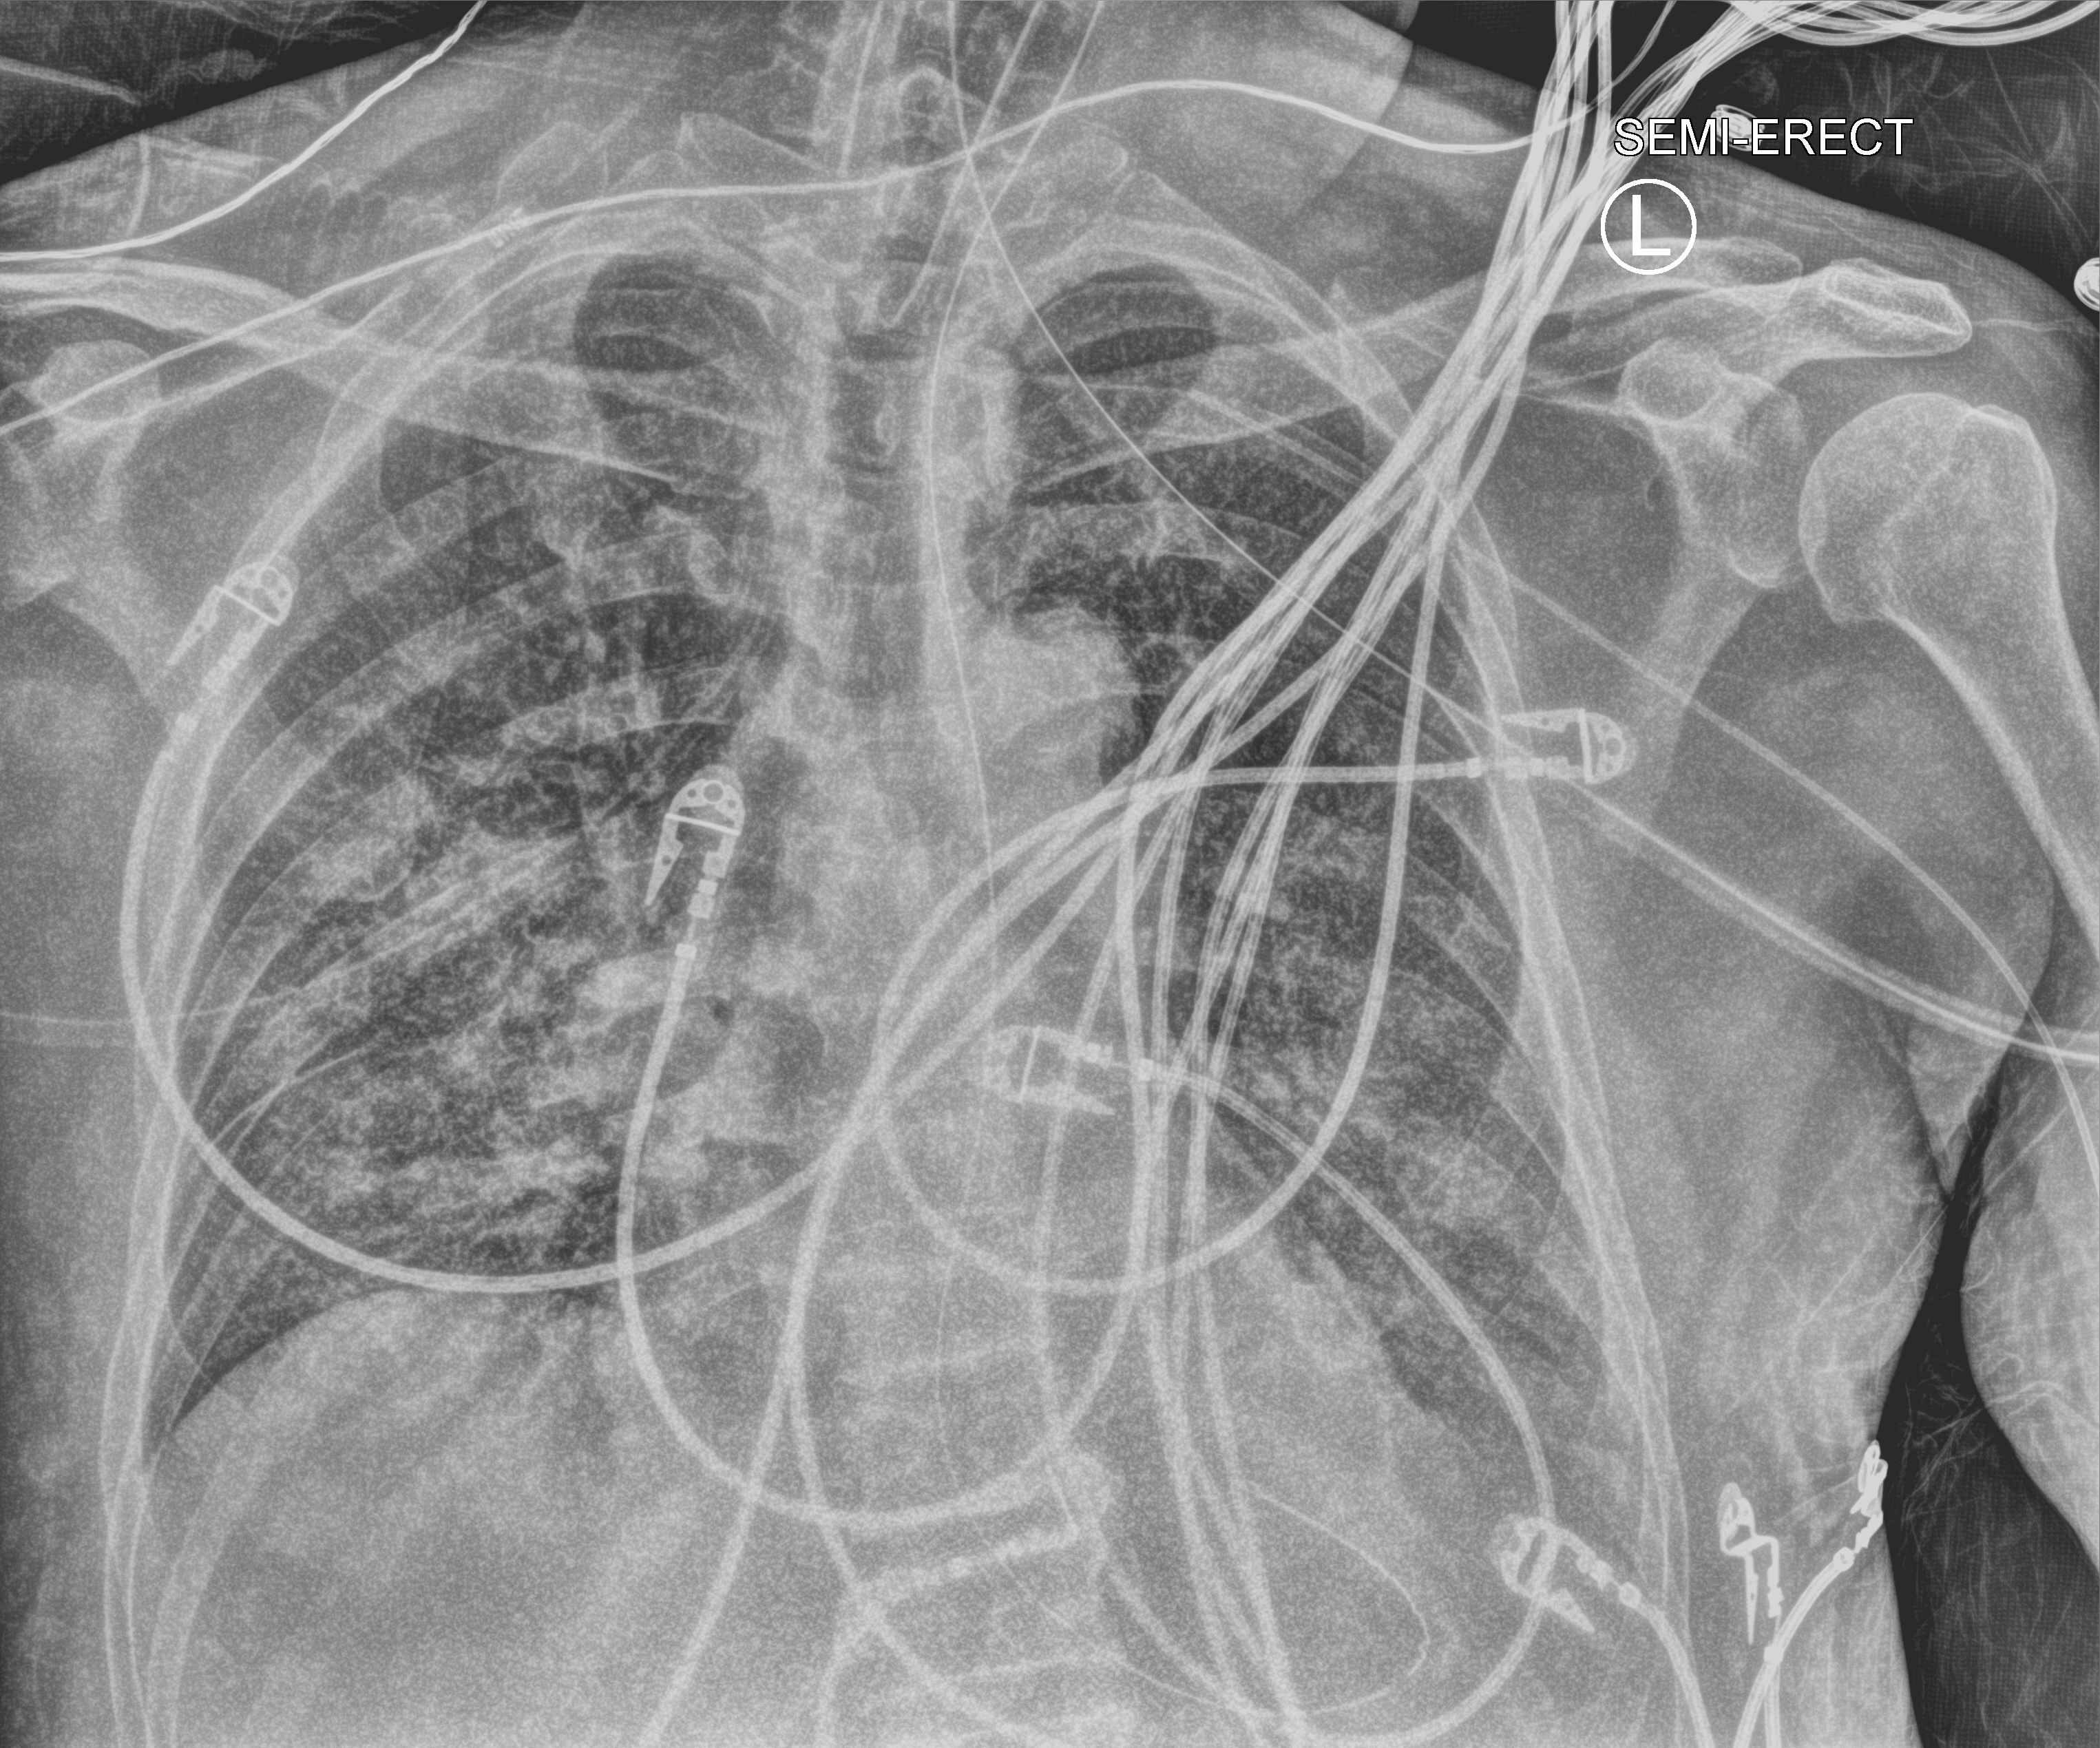
Portable chest radiograph; anteroposterior (AP) projection. Patient hospitalised with COVID-19; male, aged 60–74 years.
Hospital-stay facts (about this admission, not read from this image; timing relative to this image not recorded):
- mechanically ventilated during this hospital stay: yes